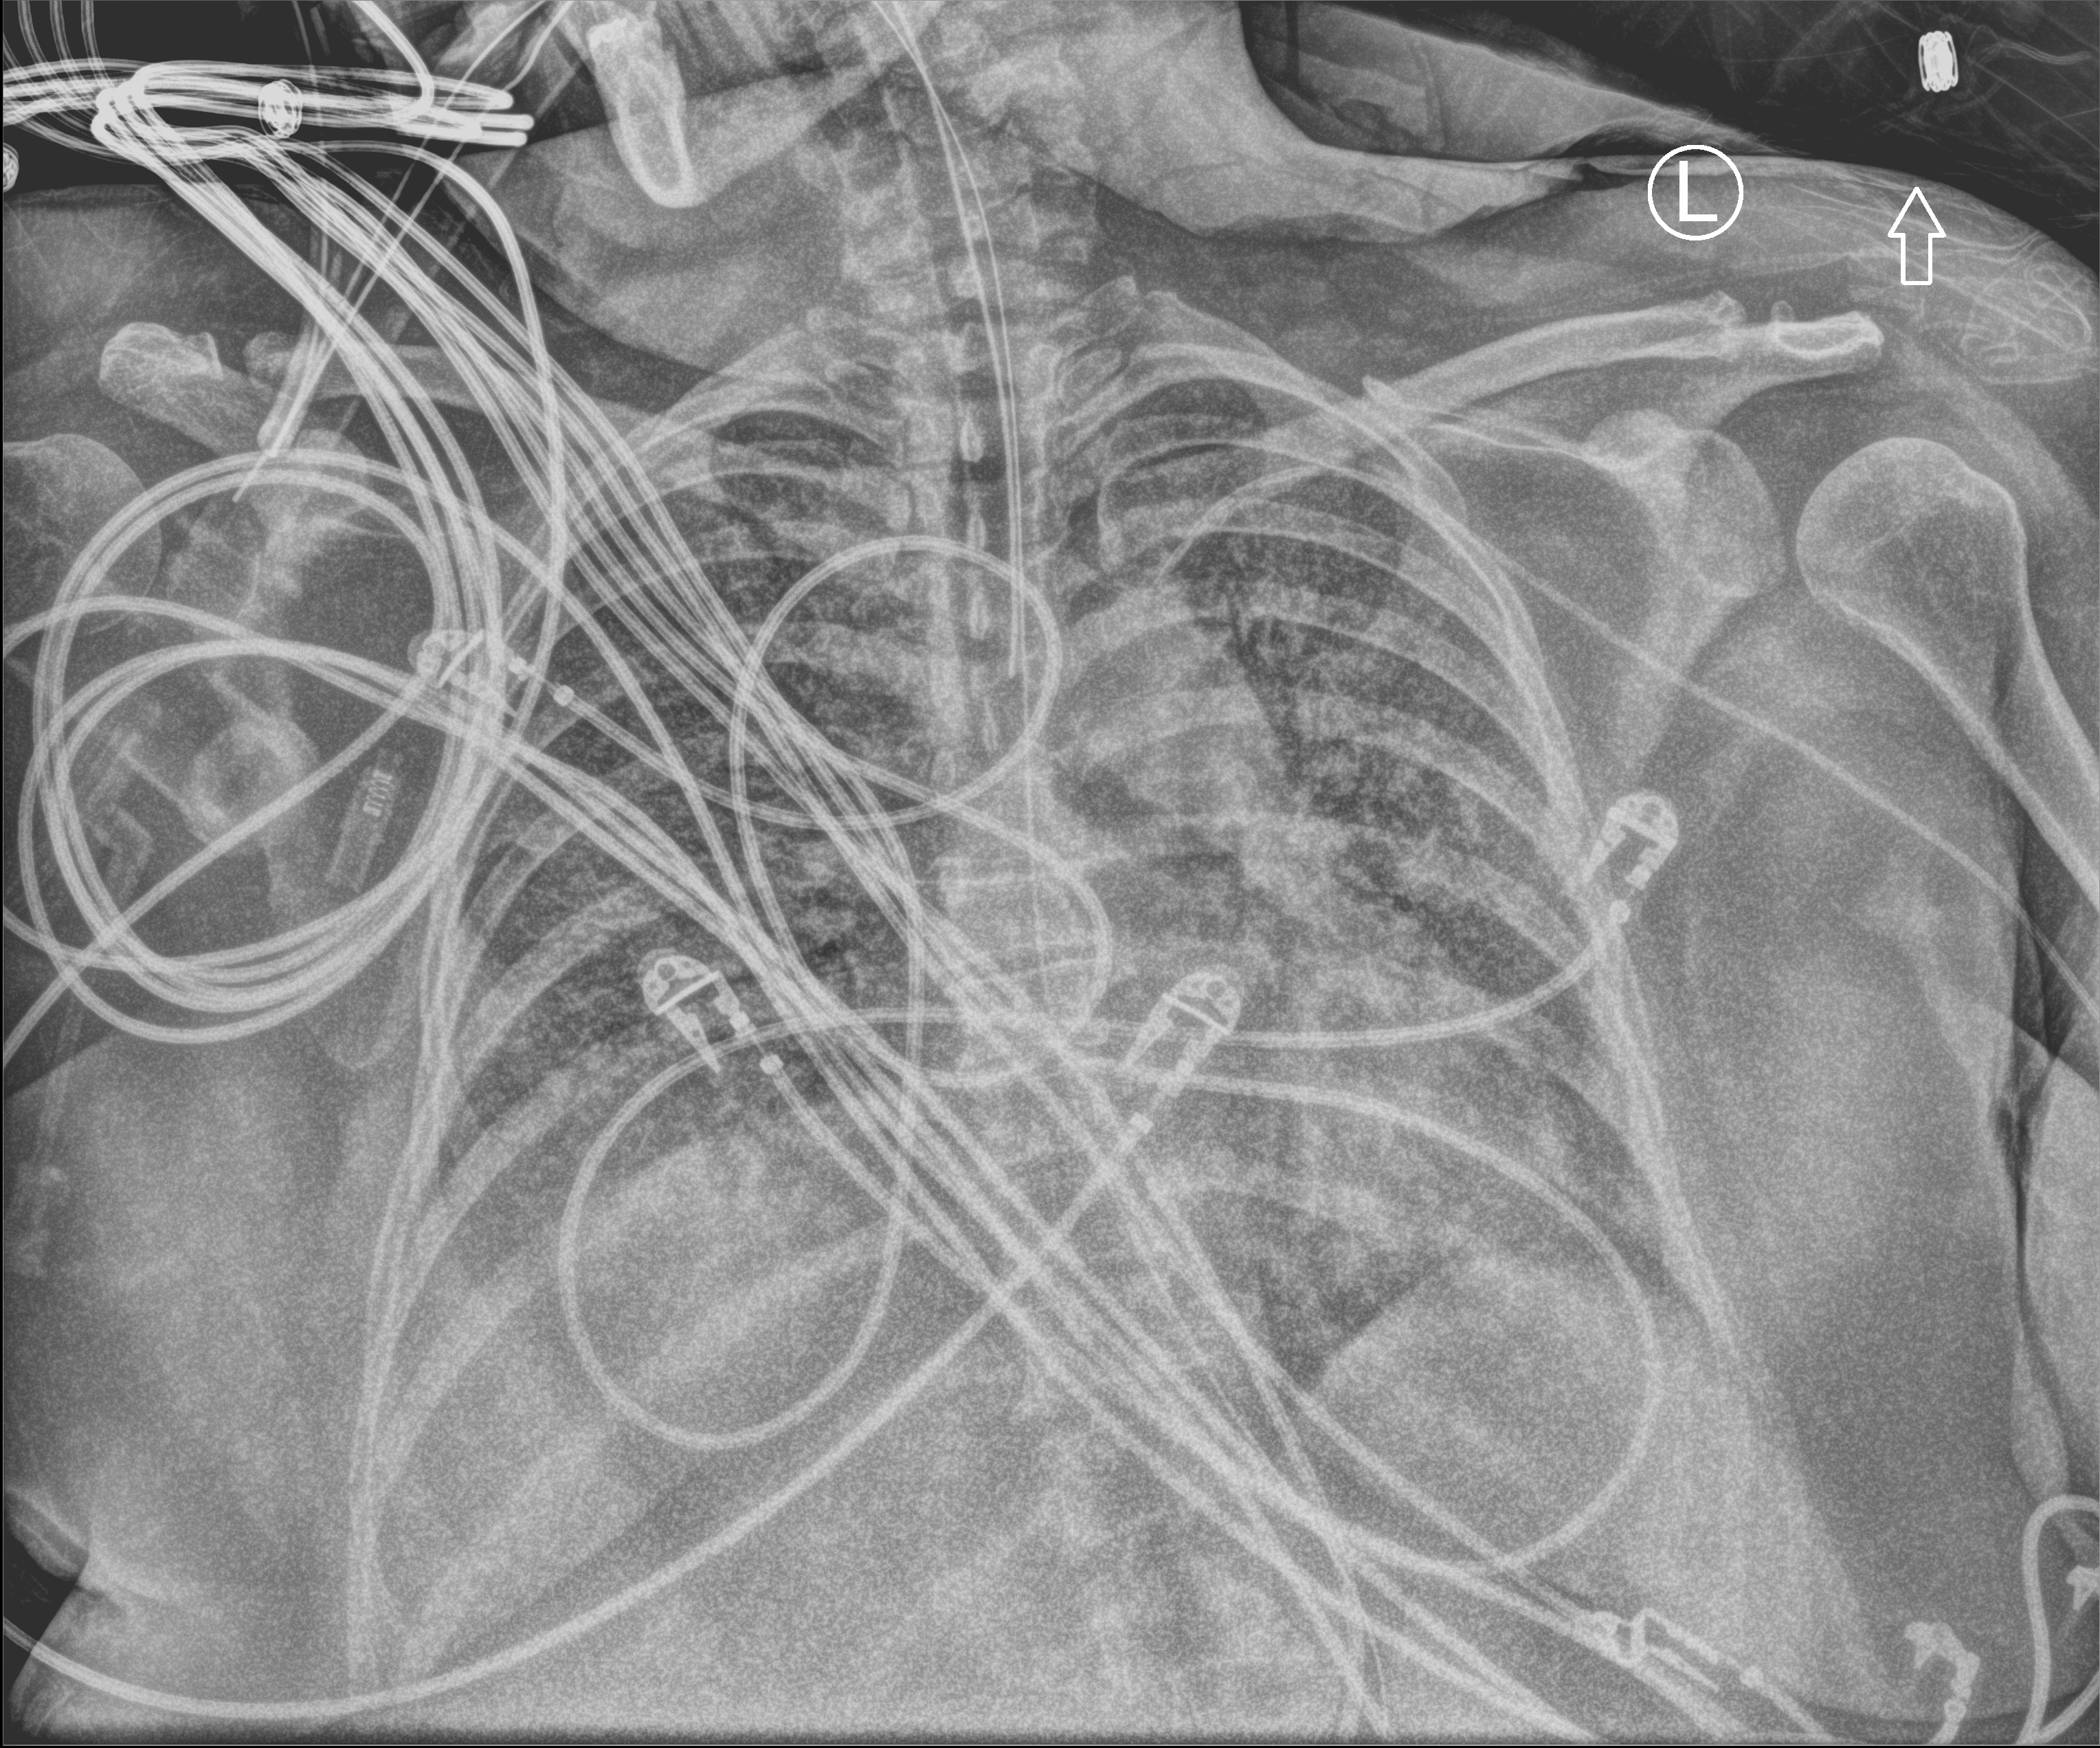
Chest X-ray (portable). Patient hospitalised with COVID-19; female, aged 18–59 years.
From the hospital-stay record, not from the radiograph (when in the stay this image was taken is not recorded): mechanically ventilated during this hospital stay: yes.